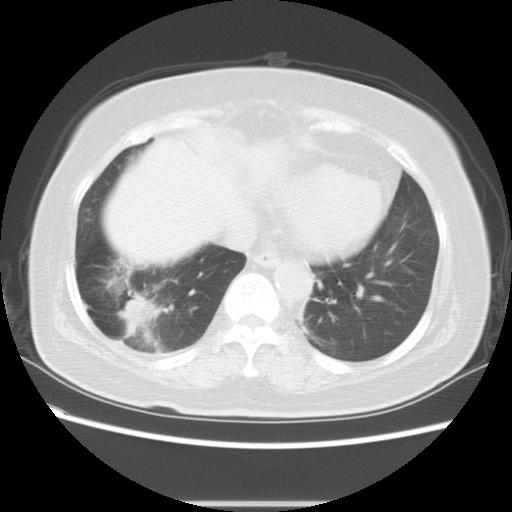
Chest CT, one axial slice; slice 20 of 61 in the series (ordered by position); 120 kVp; lung window (W 1500 / L -600 HU); 512 × 512 image matrix, field of view 350 × 350 mm. Patient: female, 65 years. Case-level facts recorded for this patient, not image findings: clinical TNM (as recorded): T2 N0 M1b.
Structures marked on this image (bounding box drawn by a radiologist):
- lung tumour (recorded histology: adenocarcinoma): box from (x=117, y=288) to (x=157, y=337) px